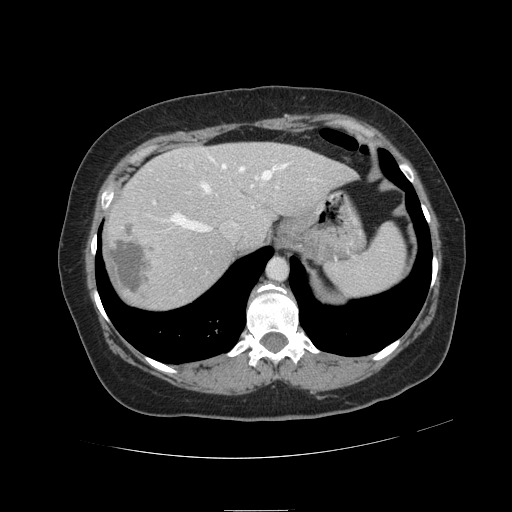
Contrast-enhanced abdominal CT, one axial slice. Position 93 of 121 along the scan axis. Intravenous contrast given. Soft-tissue window (W 400 / L 40 HU). 2.5 mm slice thickness. 512 × 512 image matrix, field of view 400 × 400 mm. Female patient, age 52 years. Case-level facts recorded for this patient, not image findings: diagnosis: colorectal cancer liver metastases, imaged before liver resection; multiple liver metastases: yes; largest metastasis: 6.3 cm; disease in both lobes: no.
Outlined on this slice (outlined manually by an expert reader):
- hepatic veins: box from (x=168, y=157) to (x=287, y=232) px
- liver: (x=105, y=143)–(x=354, y=310)
- planned liver remnant (the part of the liver to remain after resection): (x=169, y=143)–(x=354, y=245)
- portal vein (with intrahepatic branches): (x=153, y=186)–(x=279, y=204)
- liver metastasis: (x=109, y=221)–(x=155, y=296)